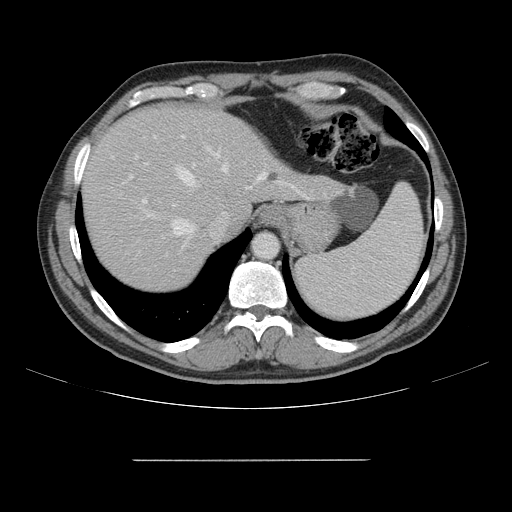
Contrast-enhanced abdominal CT, one axial slice; position 124 of 164 along the scan axis; intravenous contrast given; soft-tissue window (W 400 / L 40 HU); 2.5 mm slice thickness; 512 × 512 image matrix, field of view 404 × 404 mm. Male patient, age 54 years. Case-level facts recorded for this patient, not image findings: diagnosis: colorectal cancer liver metastases, imaged before liver resection; multiple liver metastases: yes; largest metastasis: 1 cm; chemotherapy before resection: yes.
Structures marked on this image (expert manual segmentation):
- hepatic veins: bounding box (x1, y1, x2, y2) in pixels: (172, 149, 309, 236)
- liver: (84, 107, 338, 290)
- planned liver remnant (the part of the liver to remain after resection): (83, 107, 255, 288)
- portal vein (with intrahepatic branches): (111, 136, 185, 271)
- liver metastasis: (266, 172, 280, 183)